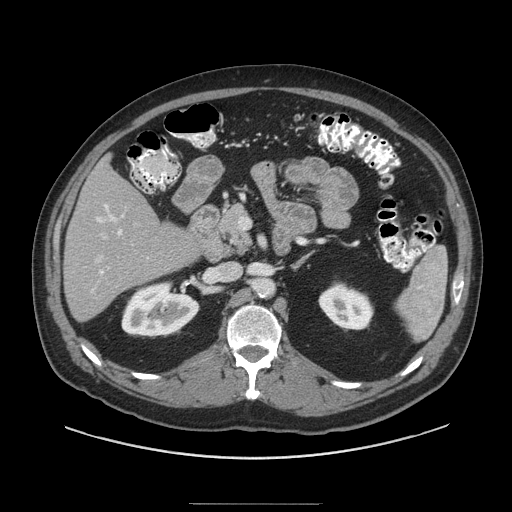
Contrast-enhanced abdominal CT (liver protocol), one axial slice; slice 45 of 91 in the series (ordered by position); 140 kVp; soft-tissue window (W 400 / L 40 HU); 2.5 mm slice thickness; 512 × 512 image matrix, field of view 440 × 440 mm. From the clinical record (not read from this slice): diagnosis: hepatocellular carcinoma (patient treated with transarterial chemoembolisation; whether this scan precedes or follows treatment is not stated here); TNM stage (as recorded): Stage-I; Child-Pugh class: A; tumour differentiation: well differentiated; tumour nodularity: uninodular.
Structures marked on this image (semi-automatic segmentation, software-assisted and operator-edited):
- liver parenchyma outside the tumour (the mass and vessels are separate outlines, so this box may not span the whole liver): bounding box <64,158,200,320> (left, top, right, bottom; pixels)
- liver vessels: <91,204,124,292>